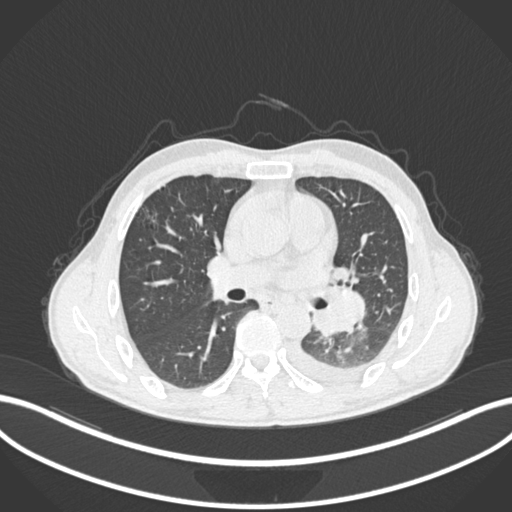
Chest CT, one axial slice. Slice 134 of 222 in the series (ordered by position). Reconstruction kernel B30f. 120 kVp. Lung window (W 1500 / L -600 HU). 512 × 512 image matrix, field of view 400 × 400 mm. Patient: male, 47 years. From the clinical record (not read from this slice): clinical TNM (as recorded): T3 N1 M1c; histopathological grade: G3.
Structures marked on this image (bounding box drawn by a radiologist):
- lung tumour (recorded histology: small cell carcinoma): box from (x=310, y=285) to (x=368, y=337) px